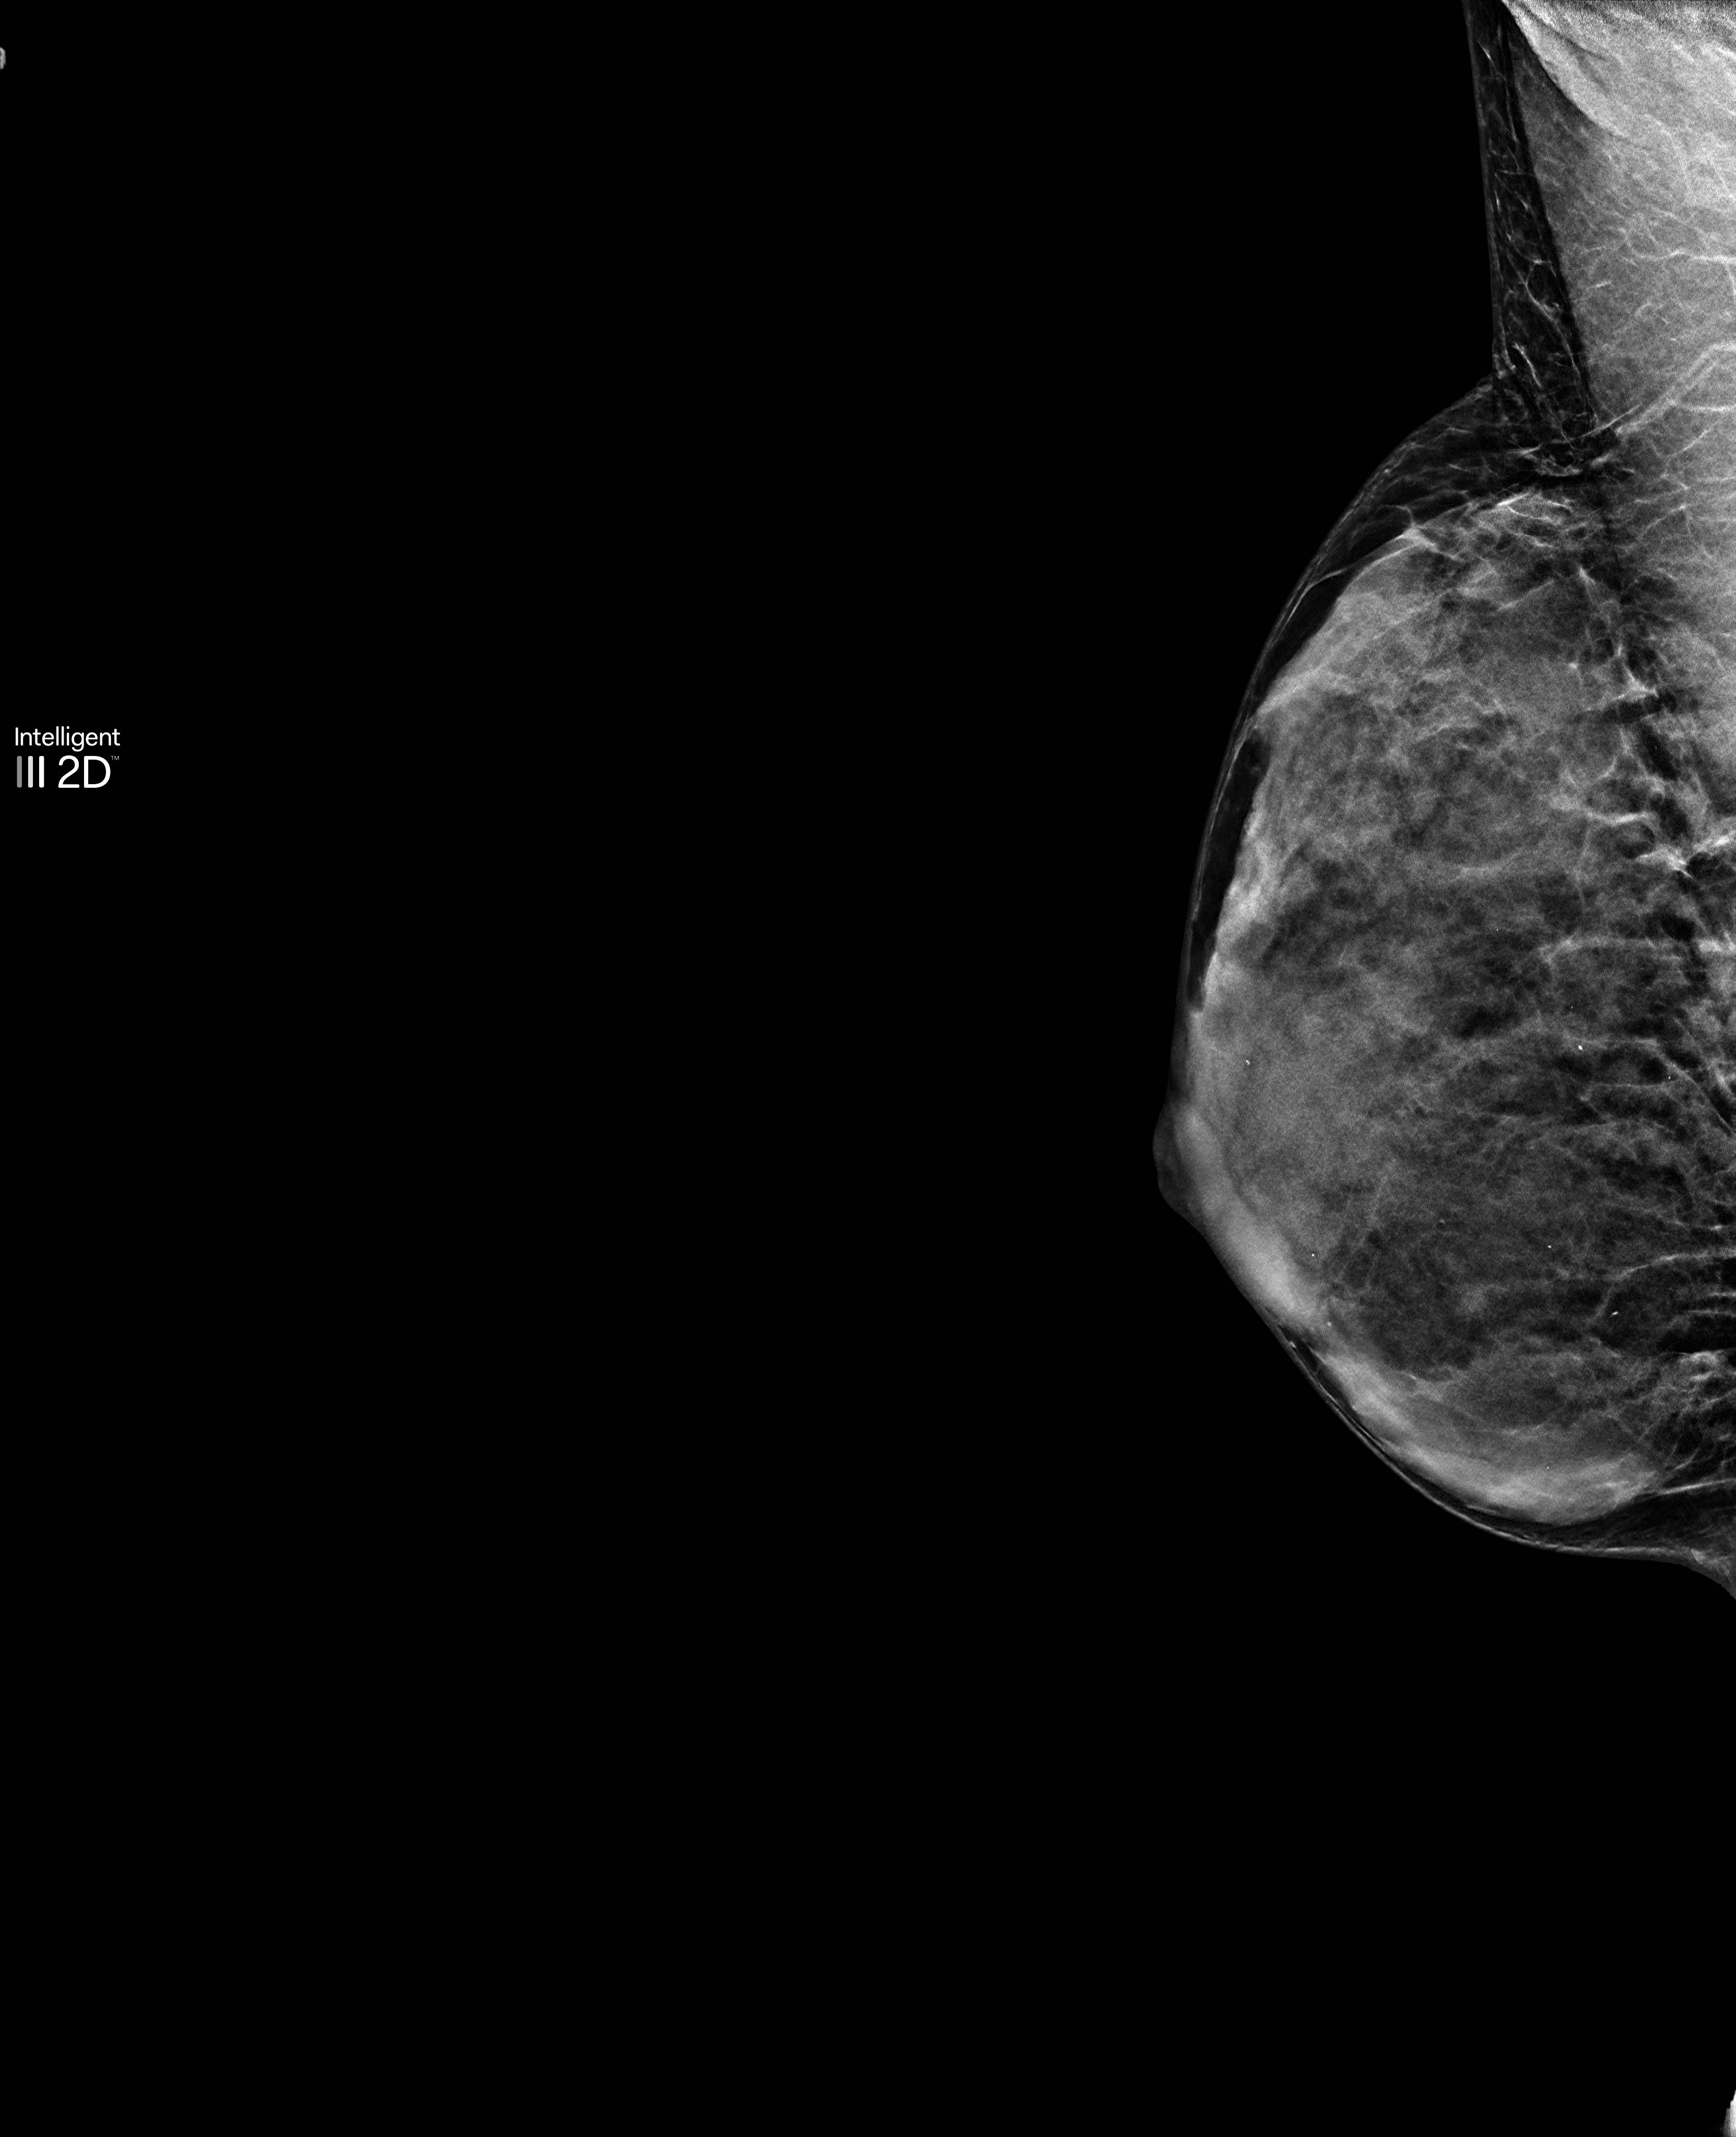
Annual screening mammography examination. Patient: female, 53 years.
Image type: synthesized 2-D view from tomosynthesis. Breast: right. Projection: MLO view.